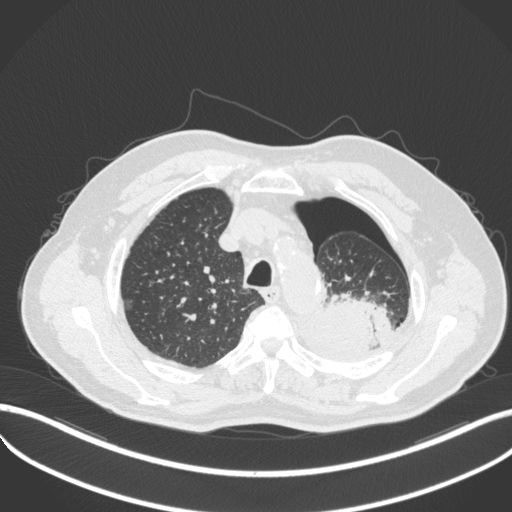
Chest CT, one axial slice; slice 399 of 466 in the series (ordered by position); reconstruction kernel B31f; 120 kVp; lung window (W 1500 / L -600 HU); 512 × 512 image matrix, field of view 400 × 400 mm. Patient: male, 76 years. Case-level facts recorded for this patient, not image findings: clinical TNM (as recorded): T3 N0 M1b.
Outlined on this slice (bounding box drawn by a radiologist):
- lung tumour (recorded histology: adenocarcinoma): bounding box (x1, y1, x2, y2) in pixels: (322, 289, 376, 358)